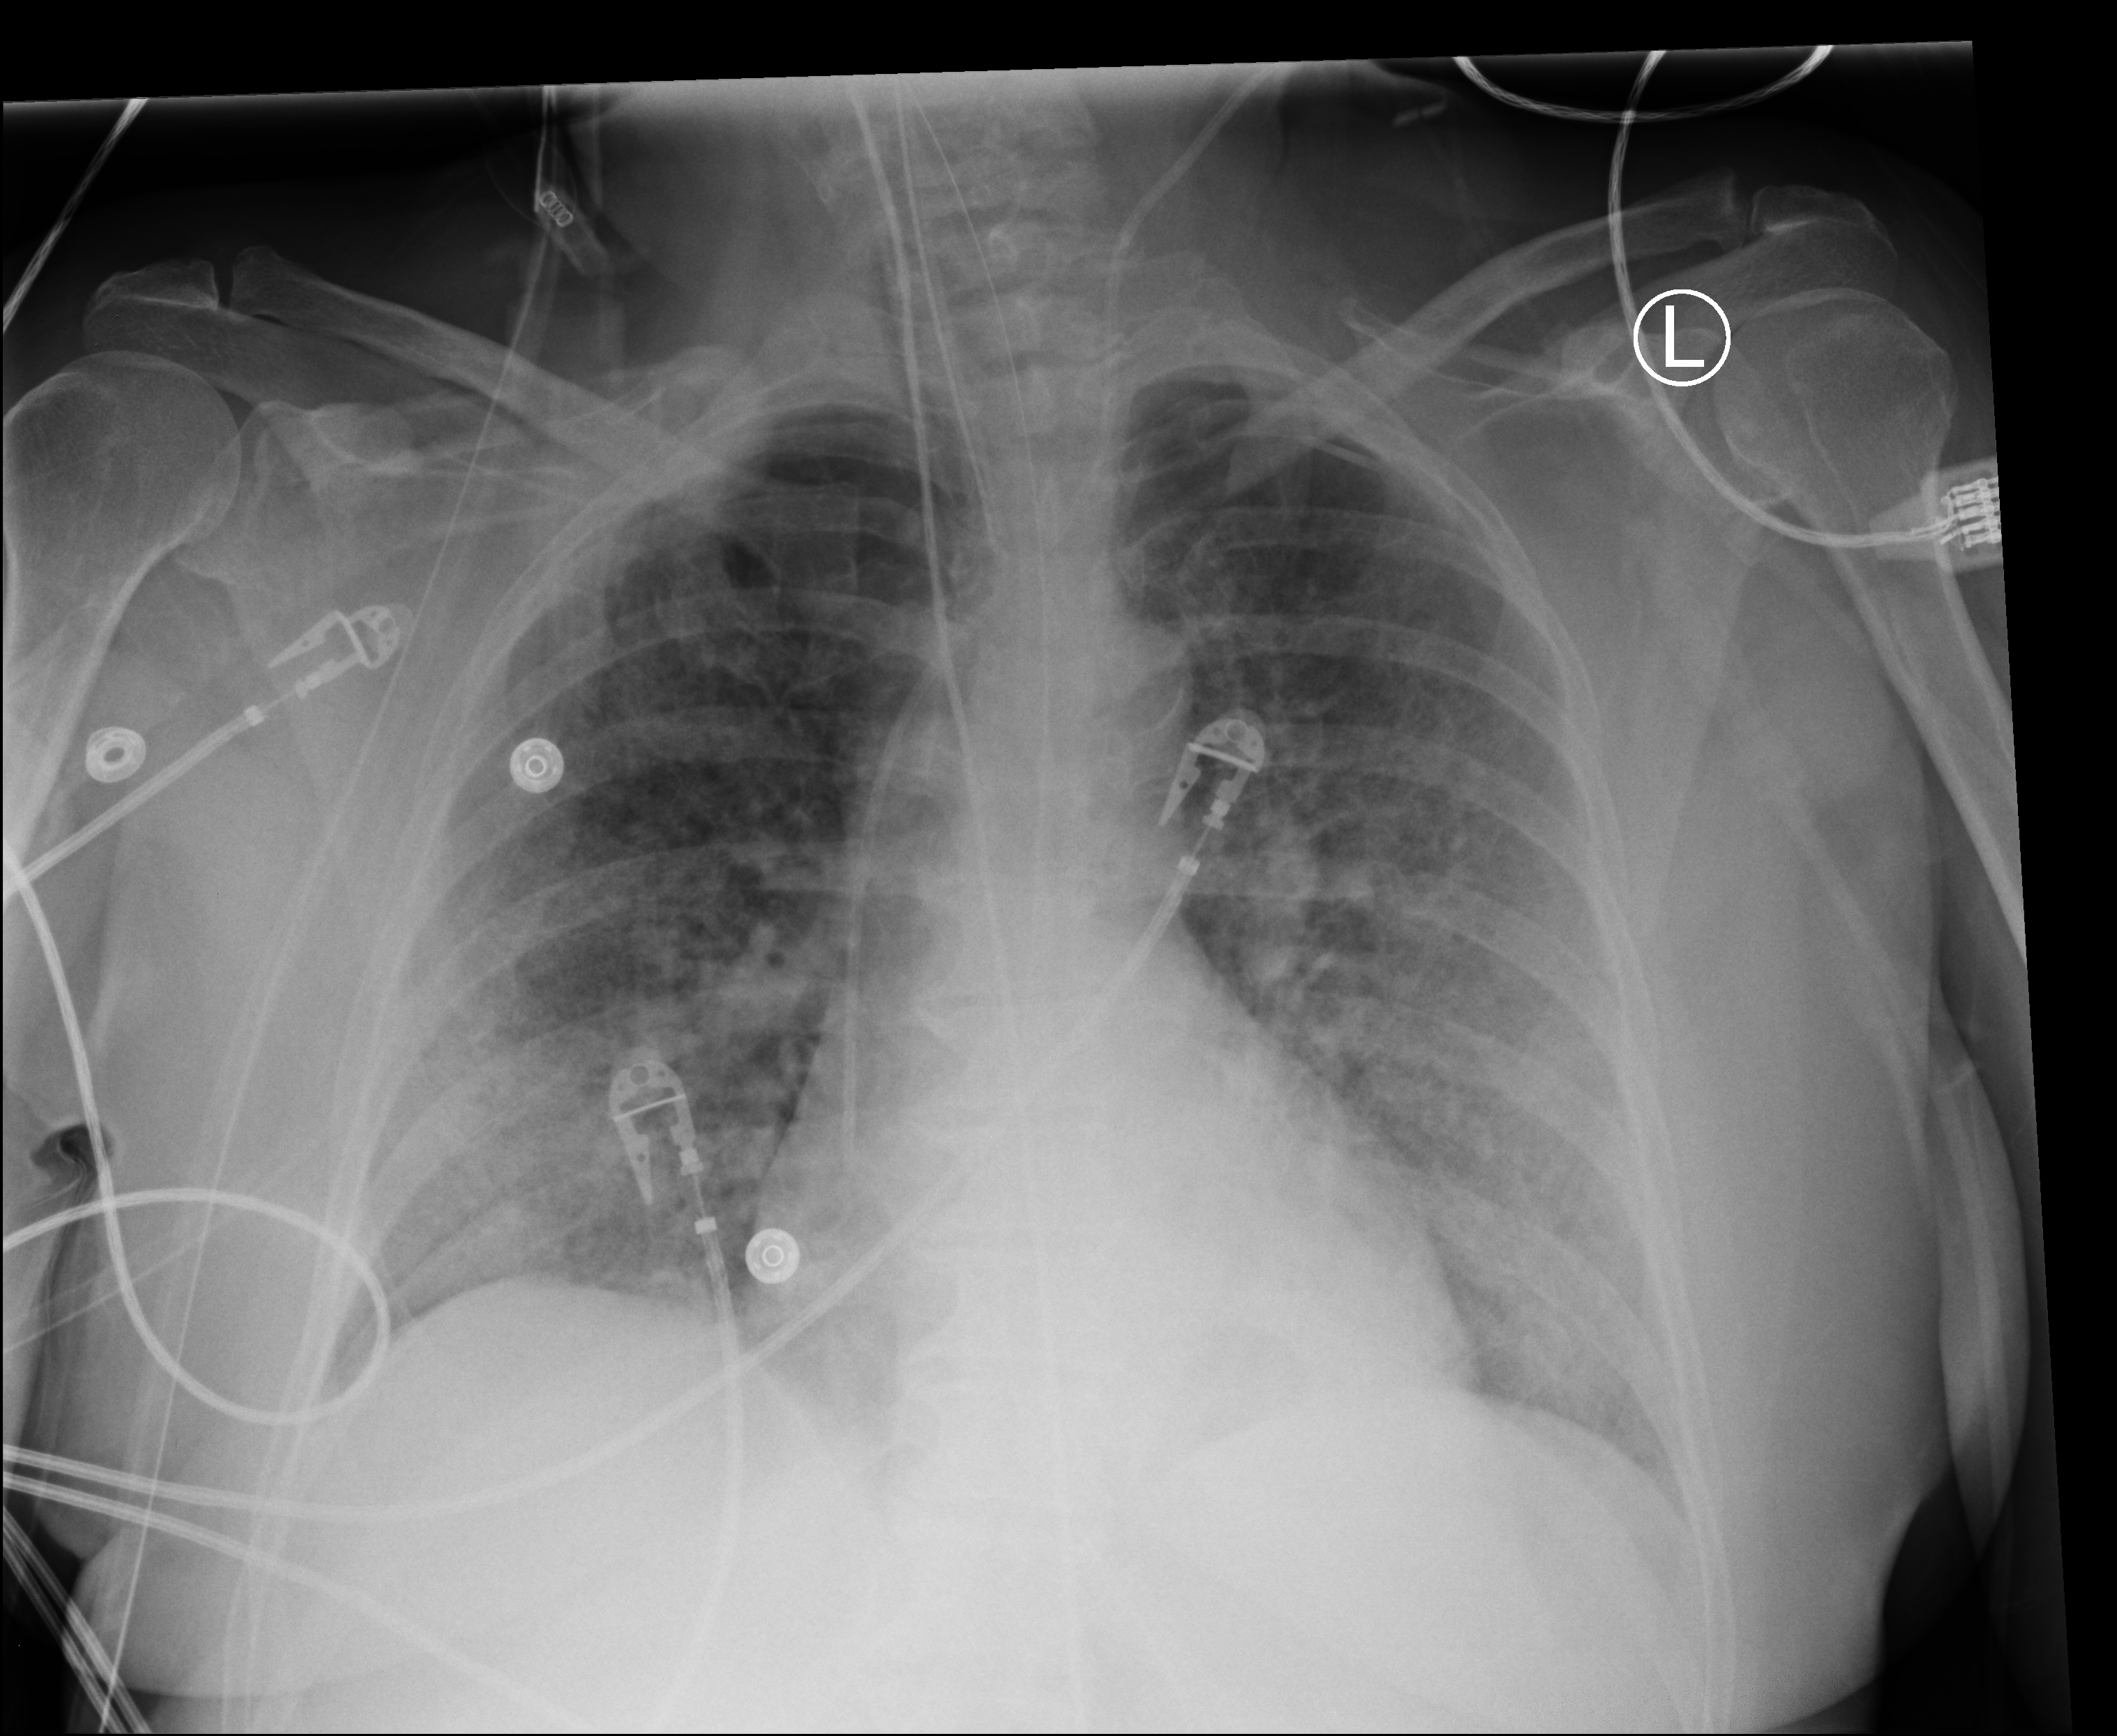
Portable chest radiograph, anteroposterior (AP) projection. Patient hospitalised with COVID-19; female, aged 60–74 years.
Hospital-stay facts (about this admission, not read from this image; timing relative to this image not recorded): admitted to intensive care during this hospital stay: yes.